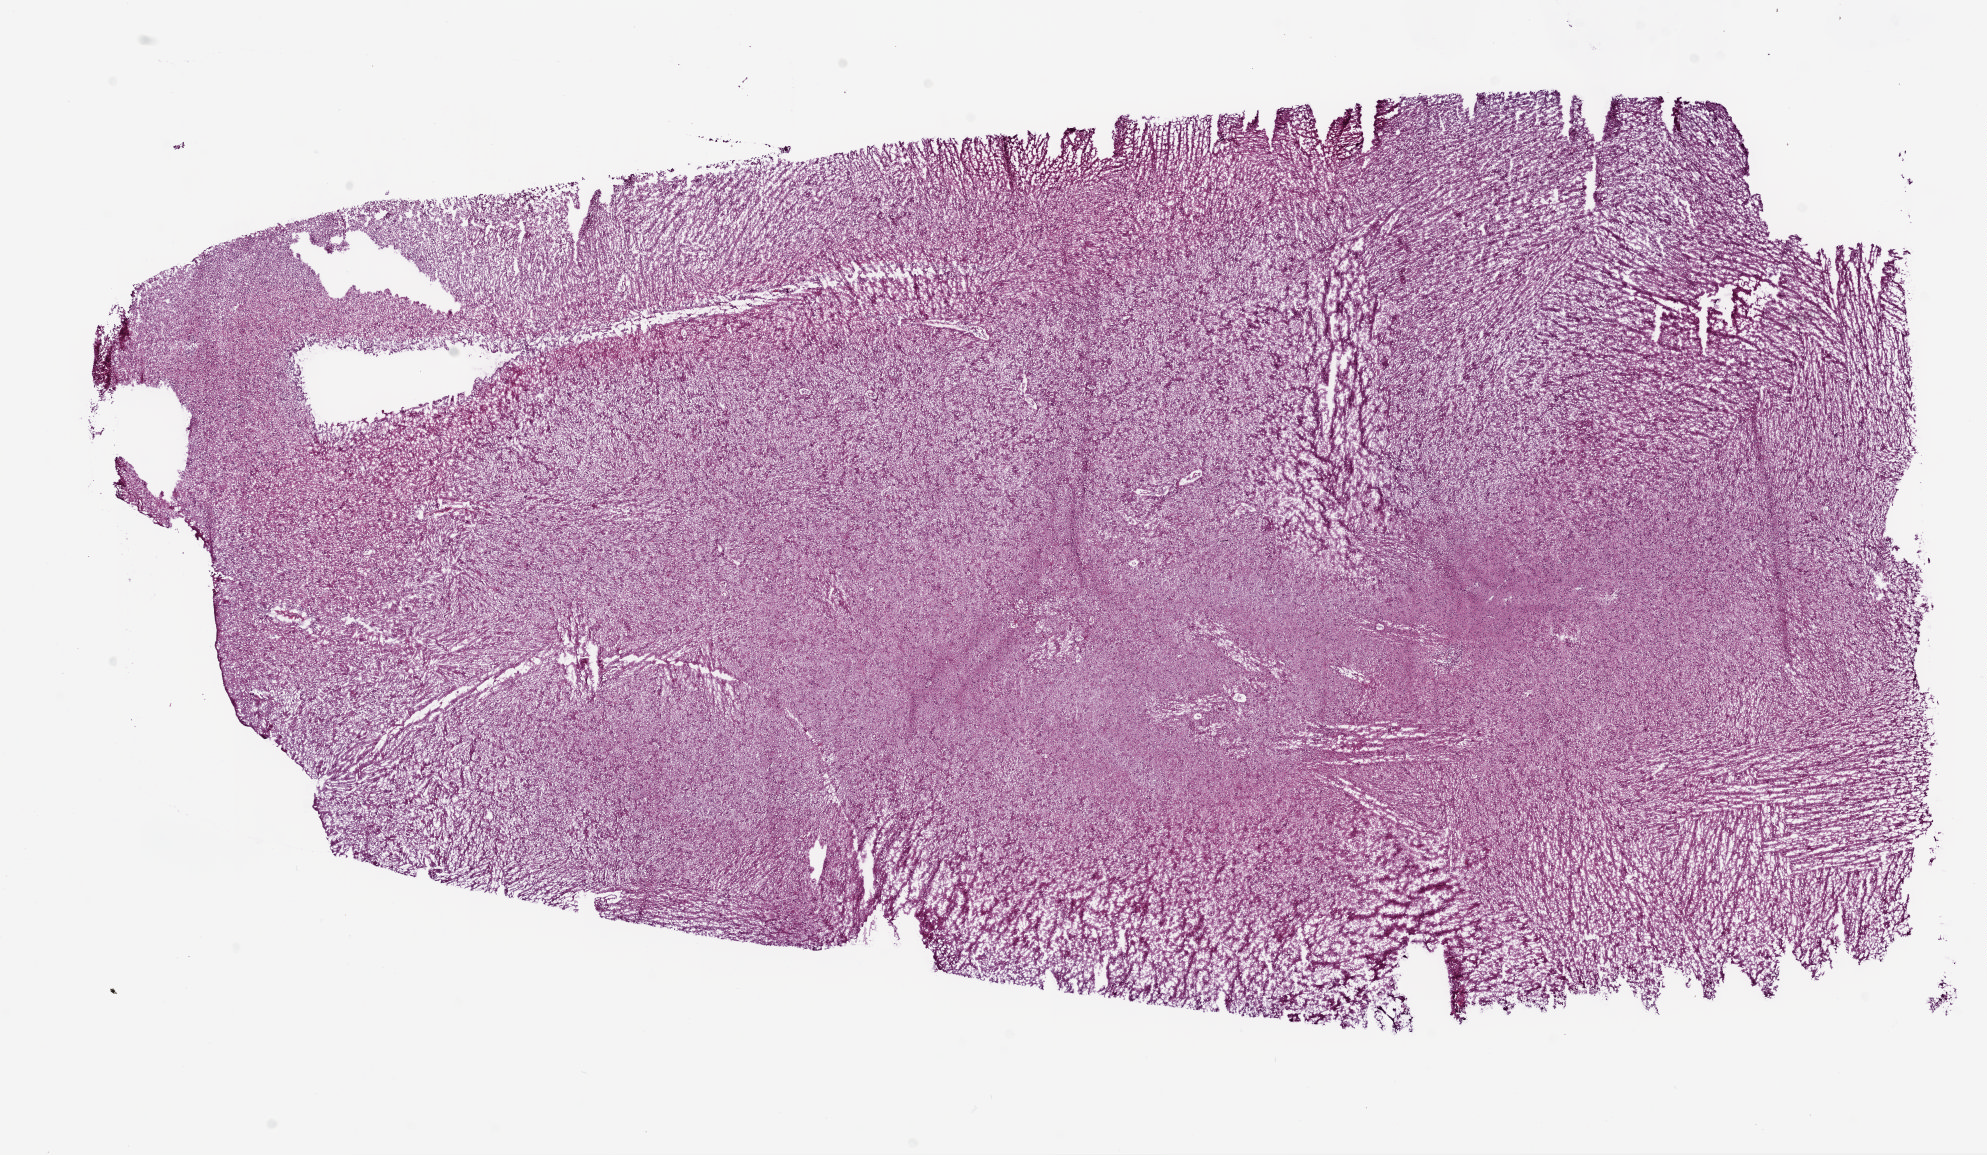
Whole-slide histology image, Hematoxylin and eosin (H&E) stained, a low-resolution overview of the entire scanned area, about 15.9 x 9.3 mm (slide scanned at 5x), frozen section from the bottom of the tissue portion, primary tumour sample from the brain. Patient: female, age at initial diagnosis 54 years. Histologic grade: G3 (poorly differentiated). Pathologist review of this section (percent, as recorded): tumour cells 100%, tumour nuclei 70%, normal cells 0%, stromal cells 0%, necrosis 0%.
Diagnosis: Astrocytoma, anaplastic. Laterality: left.